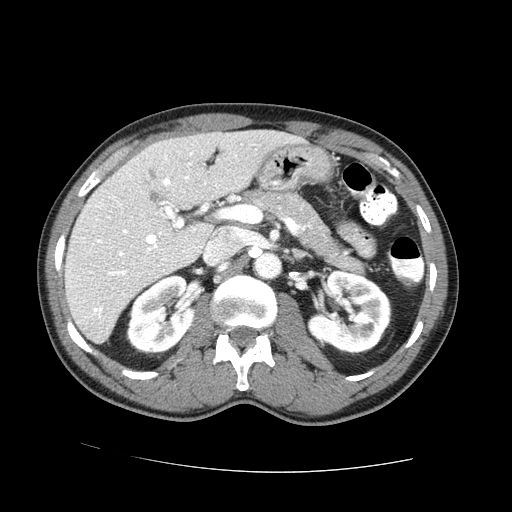
Contrast-enhanced abdominal CT (liver protocol), one axial slice; position 37 of 73 along the scan axis; one of 2 acquisitions stored at this slice position; soft-tissue window (W 400 / L 40 HU); 2.5 mm slice thickness; 512 × 512 image matrix, field of view 380 × 380 mm. Case-level facts recorded for this patient, not image findings: diagnosis: hepatocellular carcinoma (patient treated with transarterial chemoembolisation; whether this scan precedes or follows treatment is not stated here); TNM stage (as recorded): Stage-IVA; Child-Pugh class: A; tumour differentiation: no biopsy.
Annotated regions visible in this slice (semi-automatically segmented with operator editing):
- liver parenchyma outside the tumour (the mass and vessels are separate outlines, so this box may not span the whole liver): box from (x=64, y=130) to (x=306, y=342) px
- mass: (x=149, y=191)–(x=160, y=201)
- liver vessels: (x=94, y=152)–(x=217, y=317)